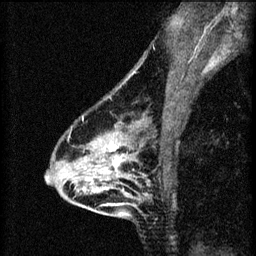
Breast MRI (dynamic contrast-enhanced), one sagittal slice. Position 43 of 60 along the scan axis. 3 images stored at this slice position (order not interpretable as contrast timing). 1.5 T. TE 4.2 ms, TR 8.2 ms. 256 × 256 image matrix. Patient: female, 46 years.
Annotated regions visible in this slice (semi-automatically segmented with operator editing):
- analysis volume of interest (the breast-tissue region the enhancement analysis was run in; not a lesion): bounding box [x1, y1, x2, y2] px = [55, 114, 148, 209]
- tumour enhancement mask (voxels above the 70 % enhancement threshold inside the analysis volume of interest): [104, 142, 126, 173]